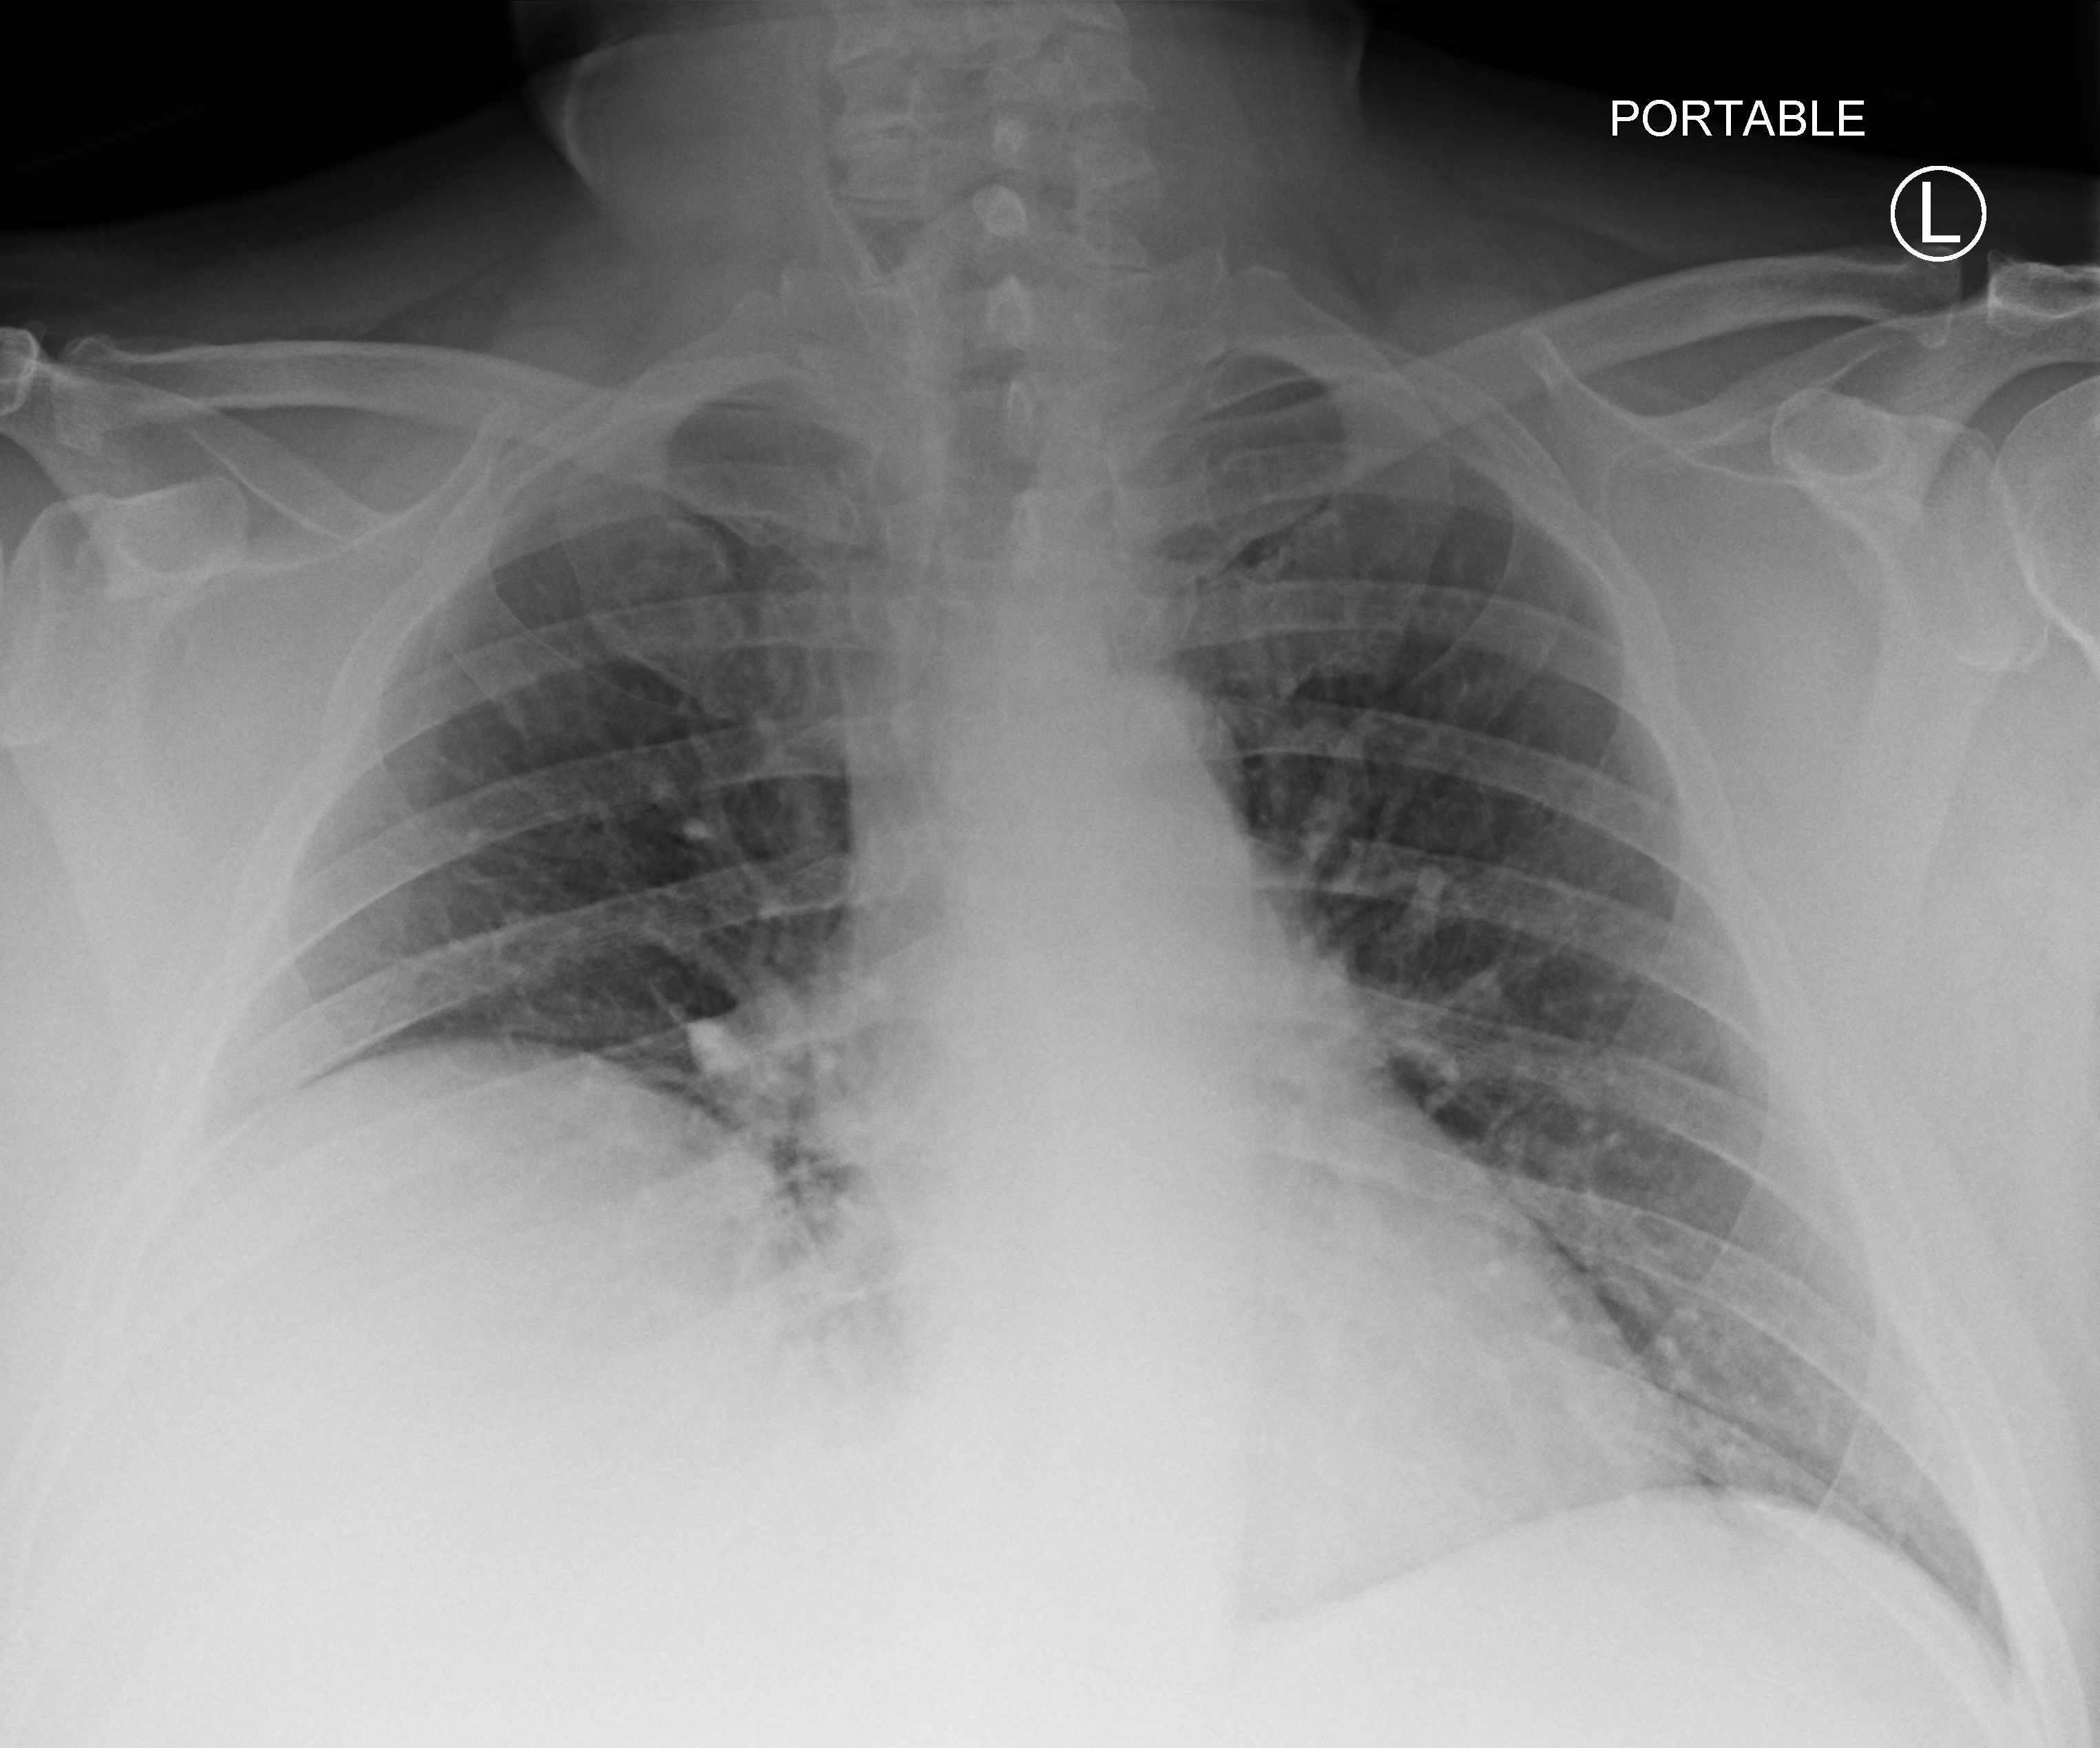
Portable chest radiograph; anteroposterior (AP) projection. Male patient hospitalised with COVID-19, age 18–59 years.
Hospital-stay facts (about this admission, not read from this image; timing relative to this image not recorded): smoking status (admission record): never; mechanically ventilated during this hospital stay: yes.